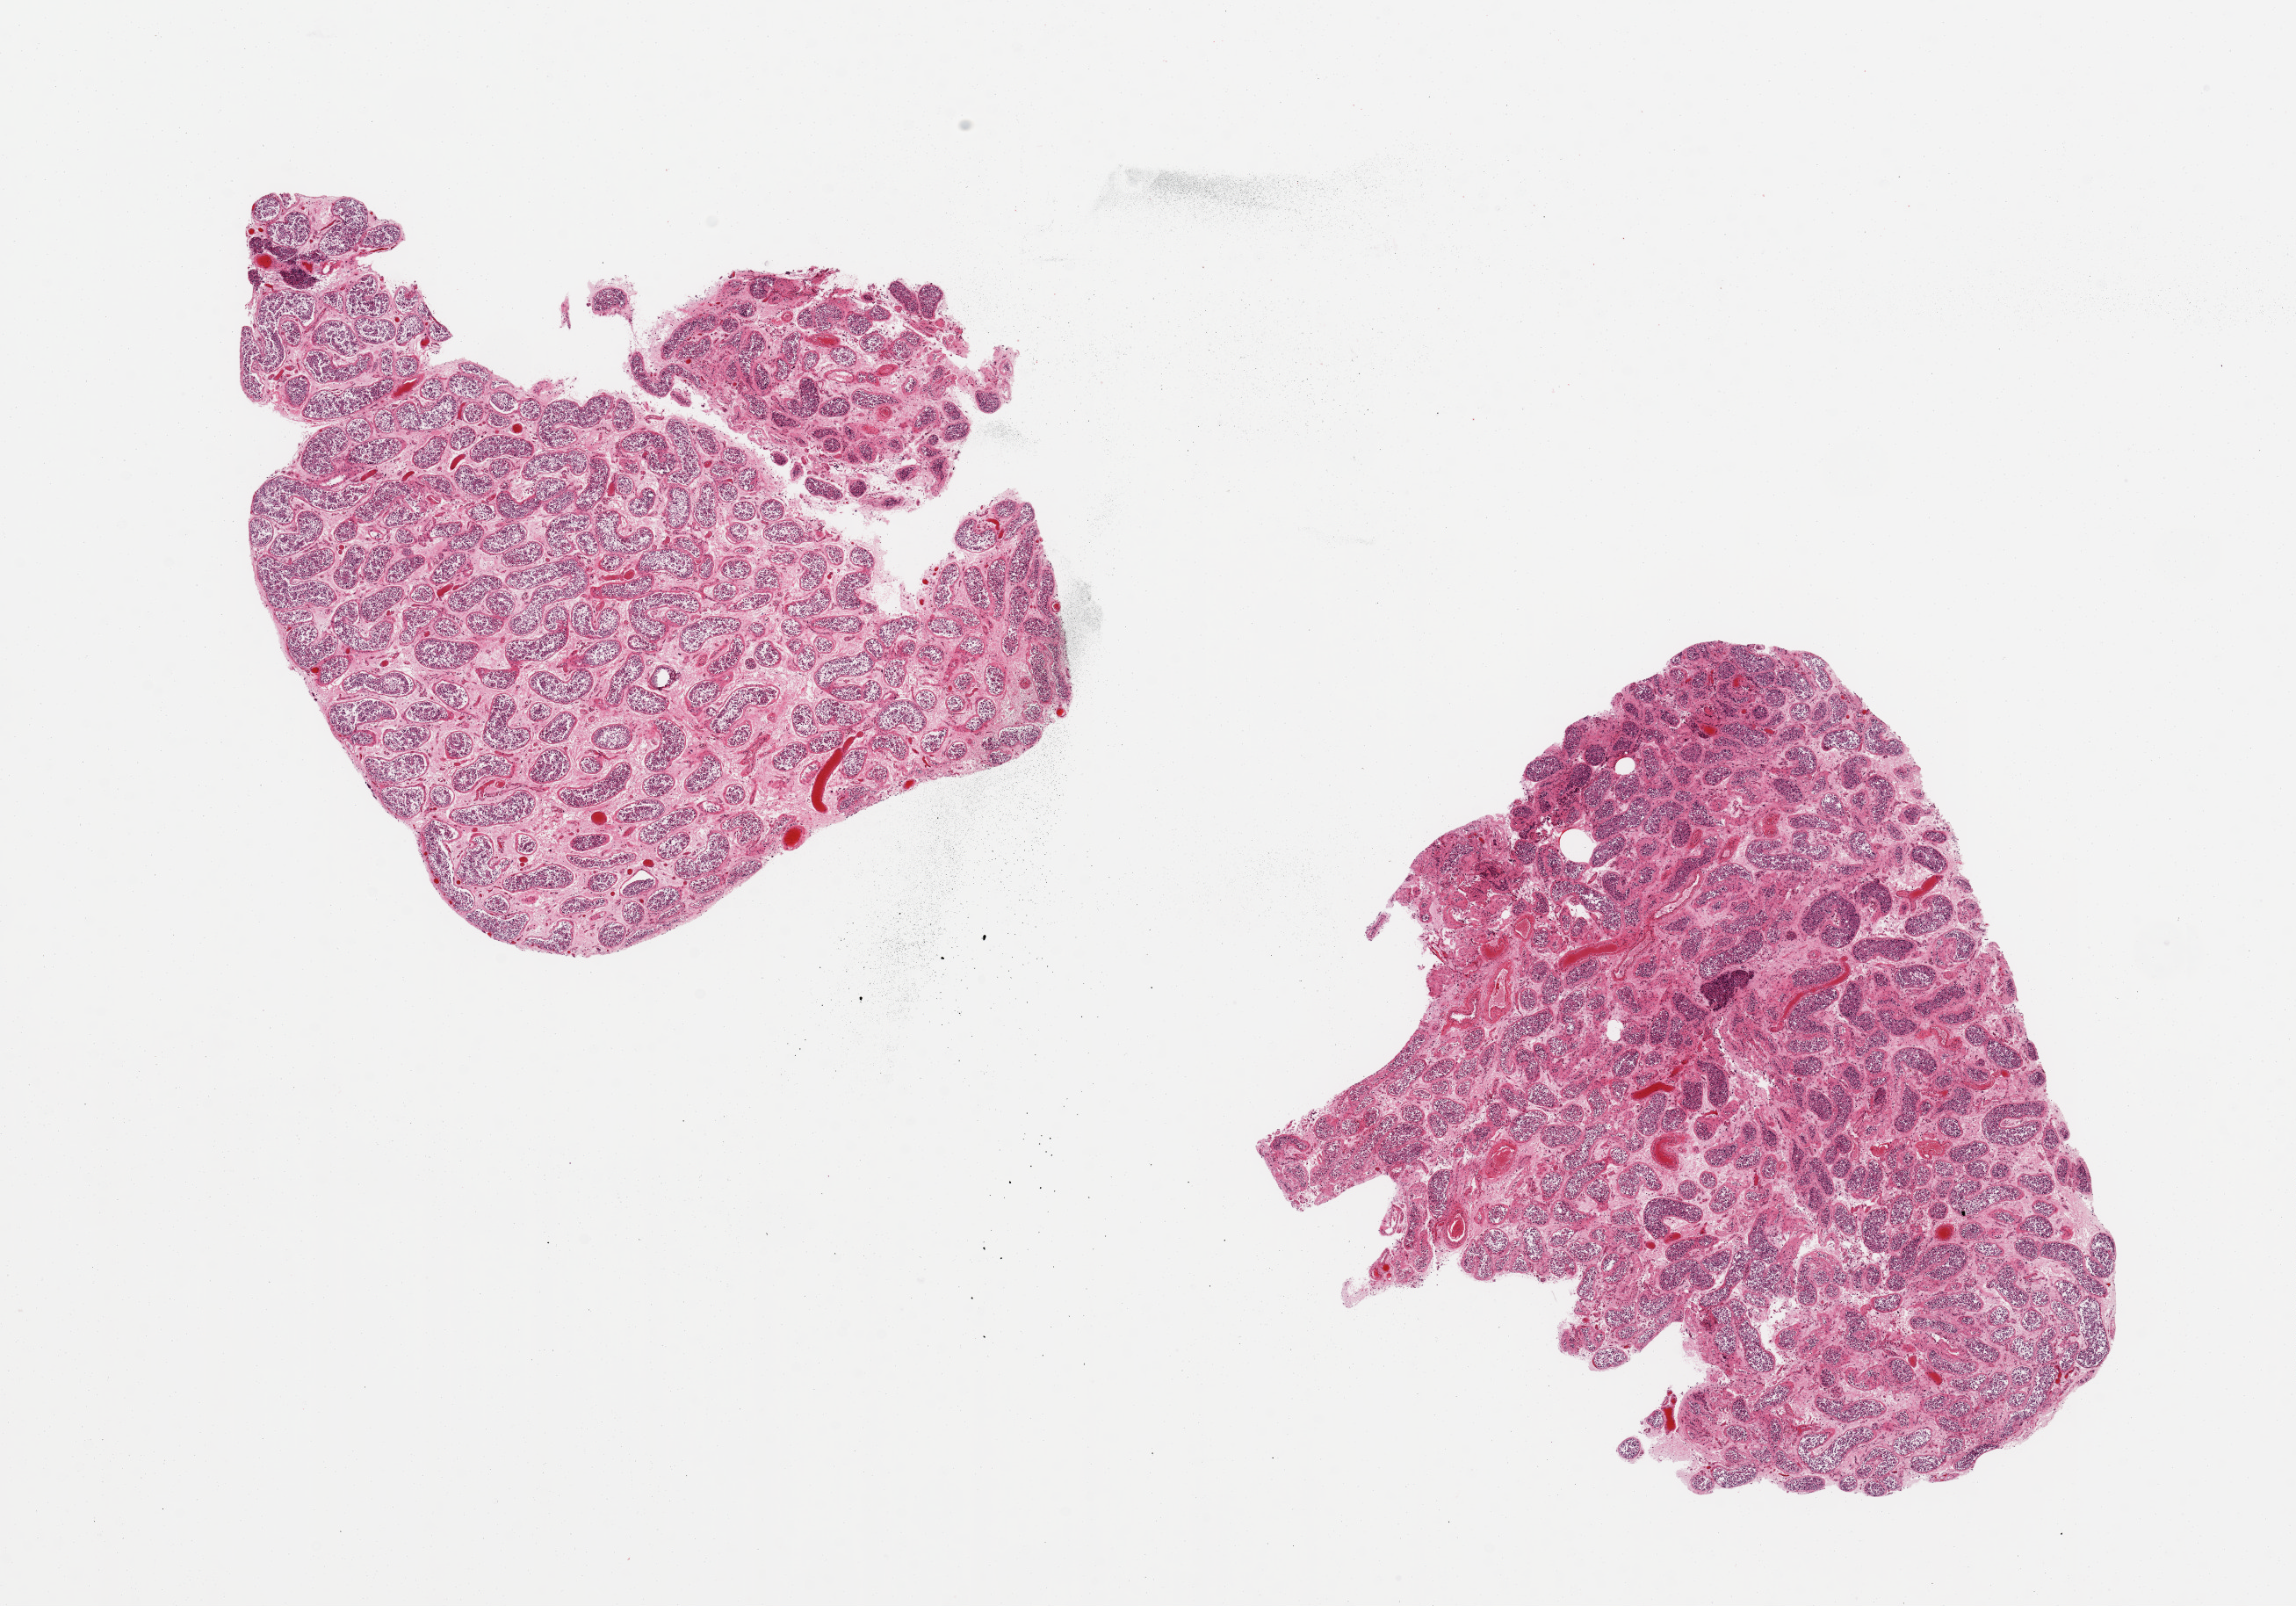
Digitized haematoxylin and eosin-stained section — low-resolution overview of the scanned area, about 20.7 x 14.5 mm, PAXgene-fixed, paraffin-embedded tissue, sampled site (target tissue): testis, tissue donor sample.
* reviewer comment on this tissue sample: 2 pieces, 7x6 & 7x7 mm; spermatogenesis